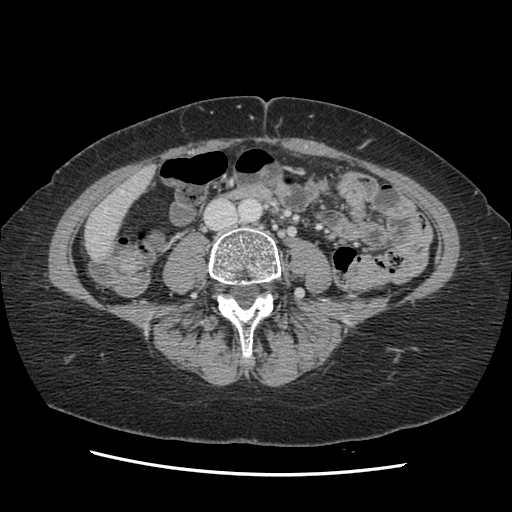
Contrast-enhanced abdominal CT, one axial slice; position 20 of 141 along the scan axis; soft-tissue window (W 400 / L 40 HU); 512 × 512 image matrix. Female patient, age 61 years. Case-level facts recorded for this patient, not image findings: diagnosis: colorectal cancer liver metastases, imaged before liver resection; multiple liver metastases: no; largest metastasis: 2.4 cm.
Annotated regions visible in this slice (manually delineated by an expert):
- hepatic veins: box from (x=95, y=209) to (x=107, y=239) px
- liver: (x=86, y=168)–(x=153, y=258)
- planned liver remnant (the part of the liver to remain after resection): (x=86, y=169)–(x=153, y=258)